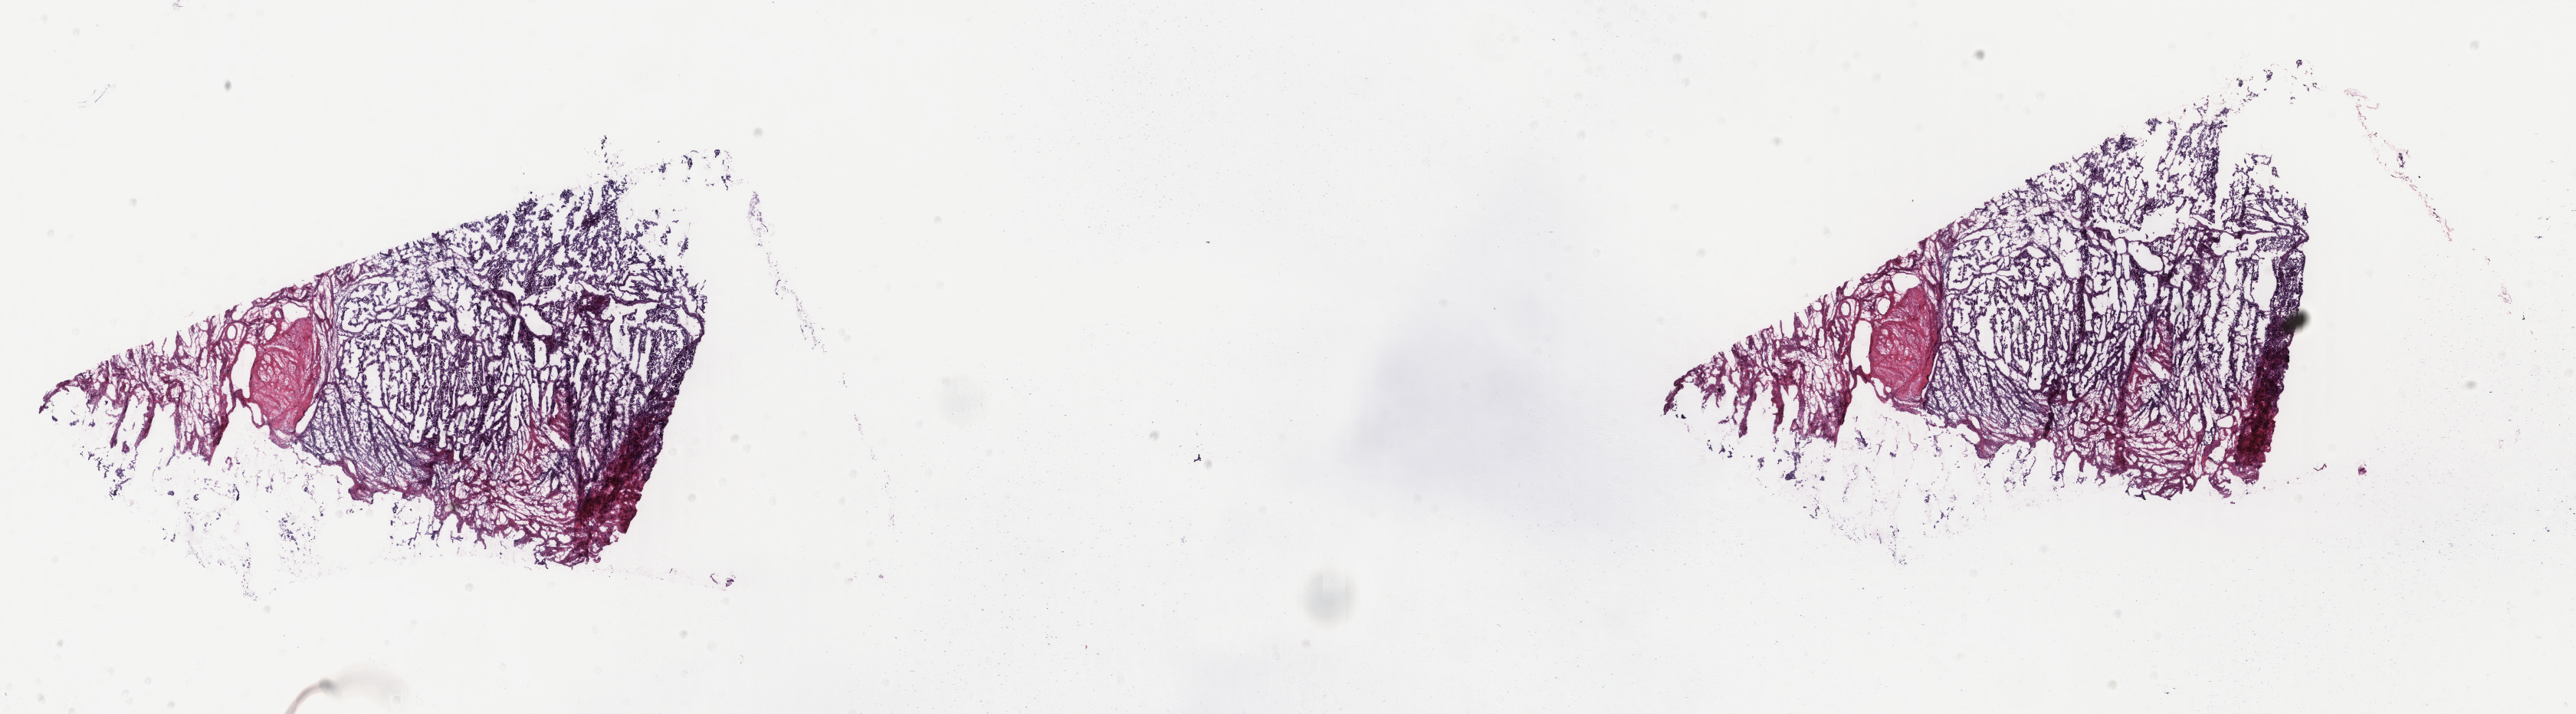
H&E whole-slide image — low-resolution overview of the scanned area, about 26.7 x 7.4 mm (from a 40x scan); frozen section; sample: primary tumour, uterus. Female patient; age at initial diagnosis 70 years. Histologic grade: G3 (poorly differentiated). Composition of this section per pathologist review: tumour cells 59%, tumour nuclei 60%, normal cells 30%, stromal cells 10%, necrosis 1%. Inflammatory infiltration, as recorded: lymphocyte infiltration 1%, monocyte infiltration 0%, neutrophil infiltration 0%.
FIGO stage: IB. Diagnosis: Serous cystadenocarcinoma, NOS.